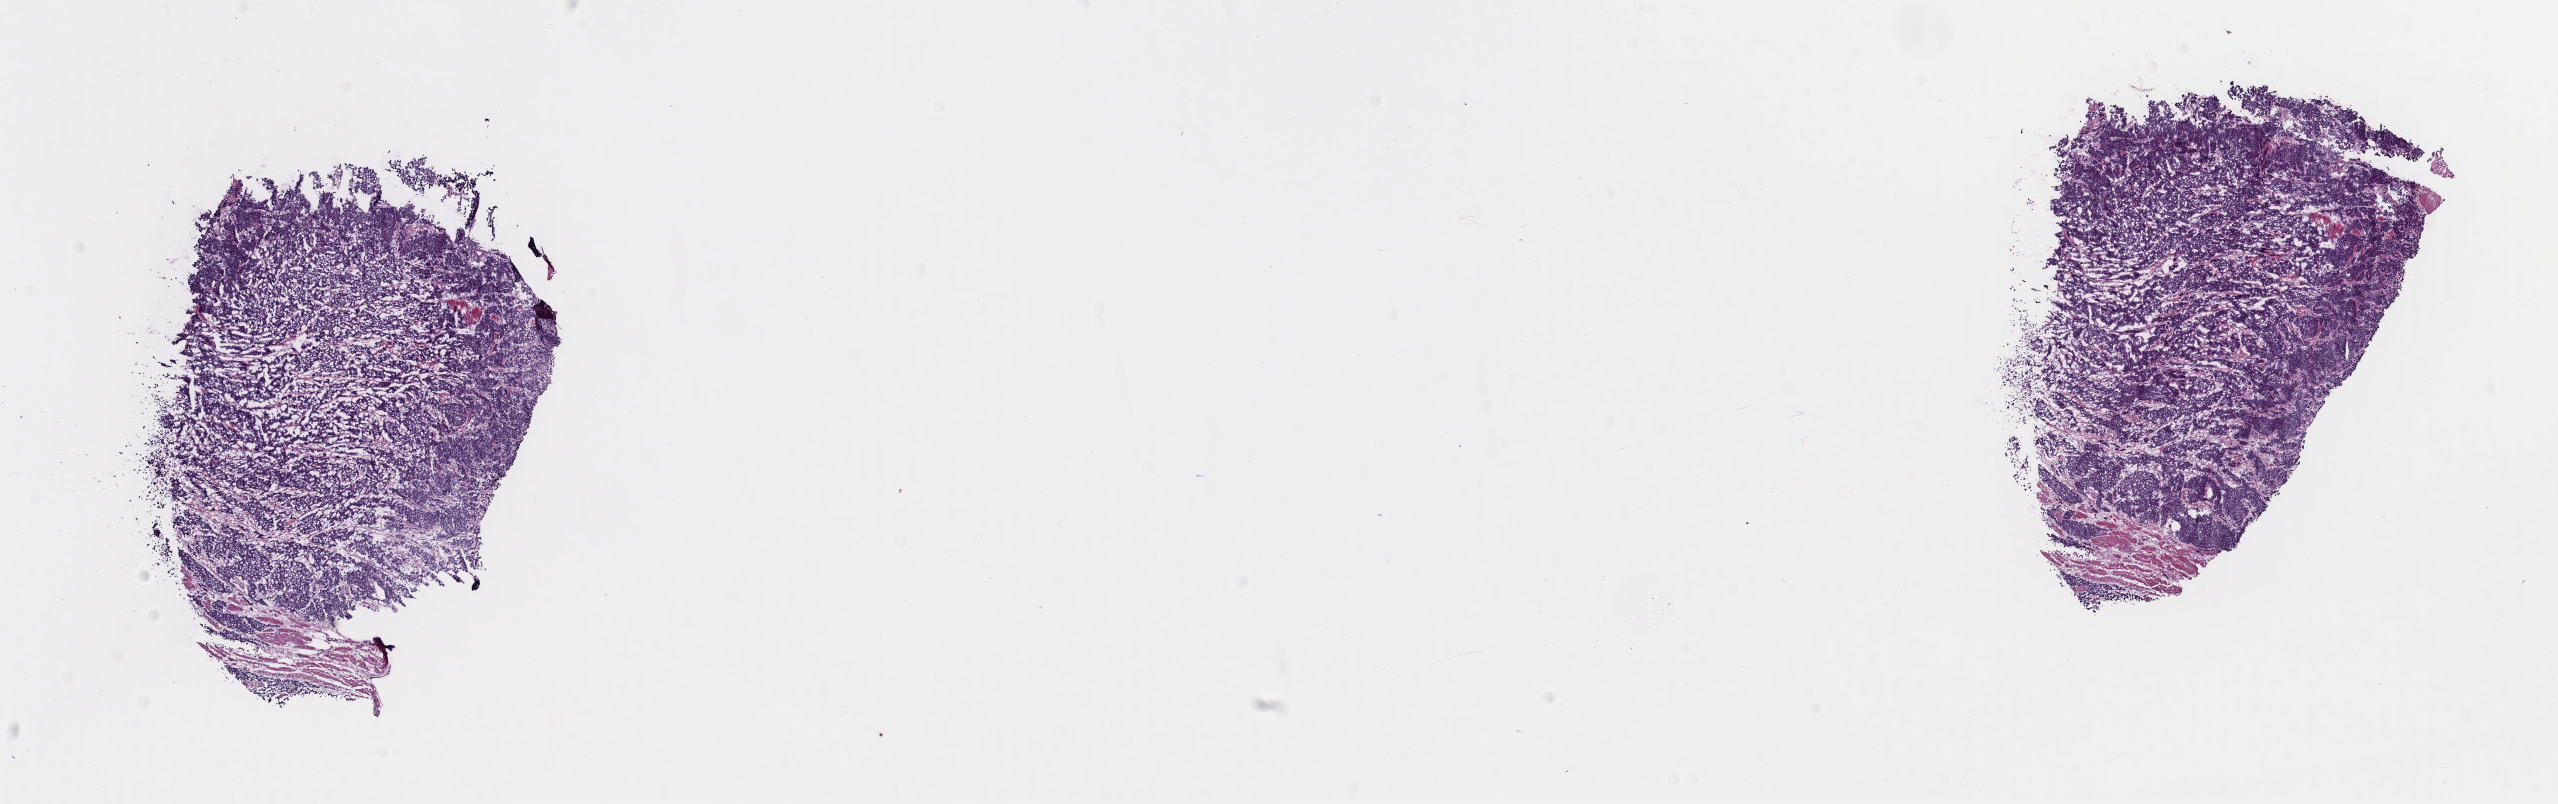
Hematoxylin and eosin (H&E) stained whole-slide image, whole scanned area (about 20.2 x 6.4 mm) shown as a low-resolution overview, frozen section from the top of the tissue portion, primary tumour sample from the esophagus. Male, age 49 years at initial diagnosis. Histologic grade: G3 (poorly differentiated). Slide review estimates, as recorded: tumour cells 80%, tumour nuclei 80%, normal cells 0%, stromal cells 20%, necrosis 0%. Infiltration values recorded for this section: lymphocyte infiltration 2%, monocyte infiltration 1%, neutrophil infiltration 1%.
AJCC pathologic stage: IIA (6th edition). Pathologic diagnosis: Squamous cell carcinoma, NOS (middle third of esophagus).